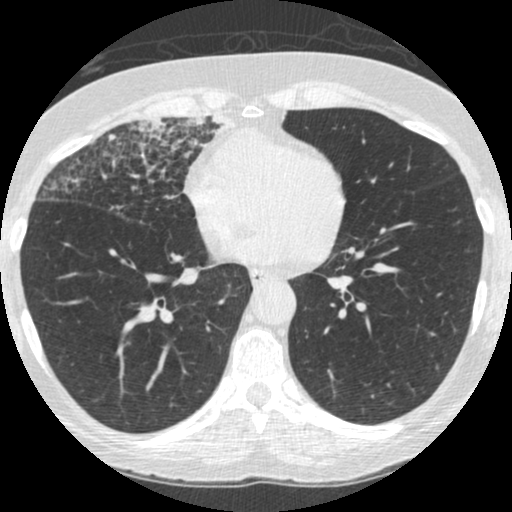
Low-dose screening chest CT, one axial slice. Position 113 of 253 along the scan axis. Lung window (W 1500 / L -600 HU). 512 × 512 image matrix, field of view 294 × 294 mm.
Annotated regions visible in this slice (outlined manually by an expert reader):
- lesion 4 (tumor, upper lobe of right lung): box from (x=180, y=115) to (x=228, y=147) px